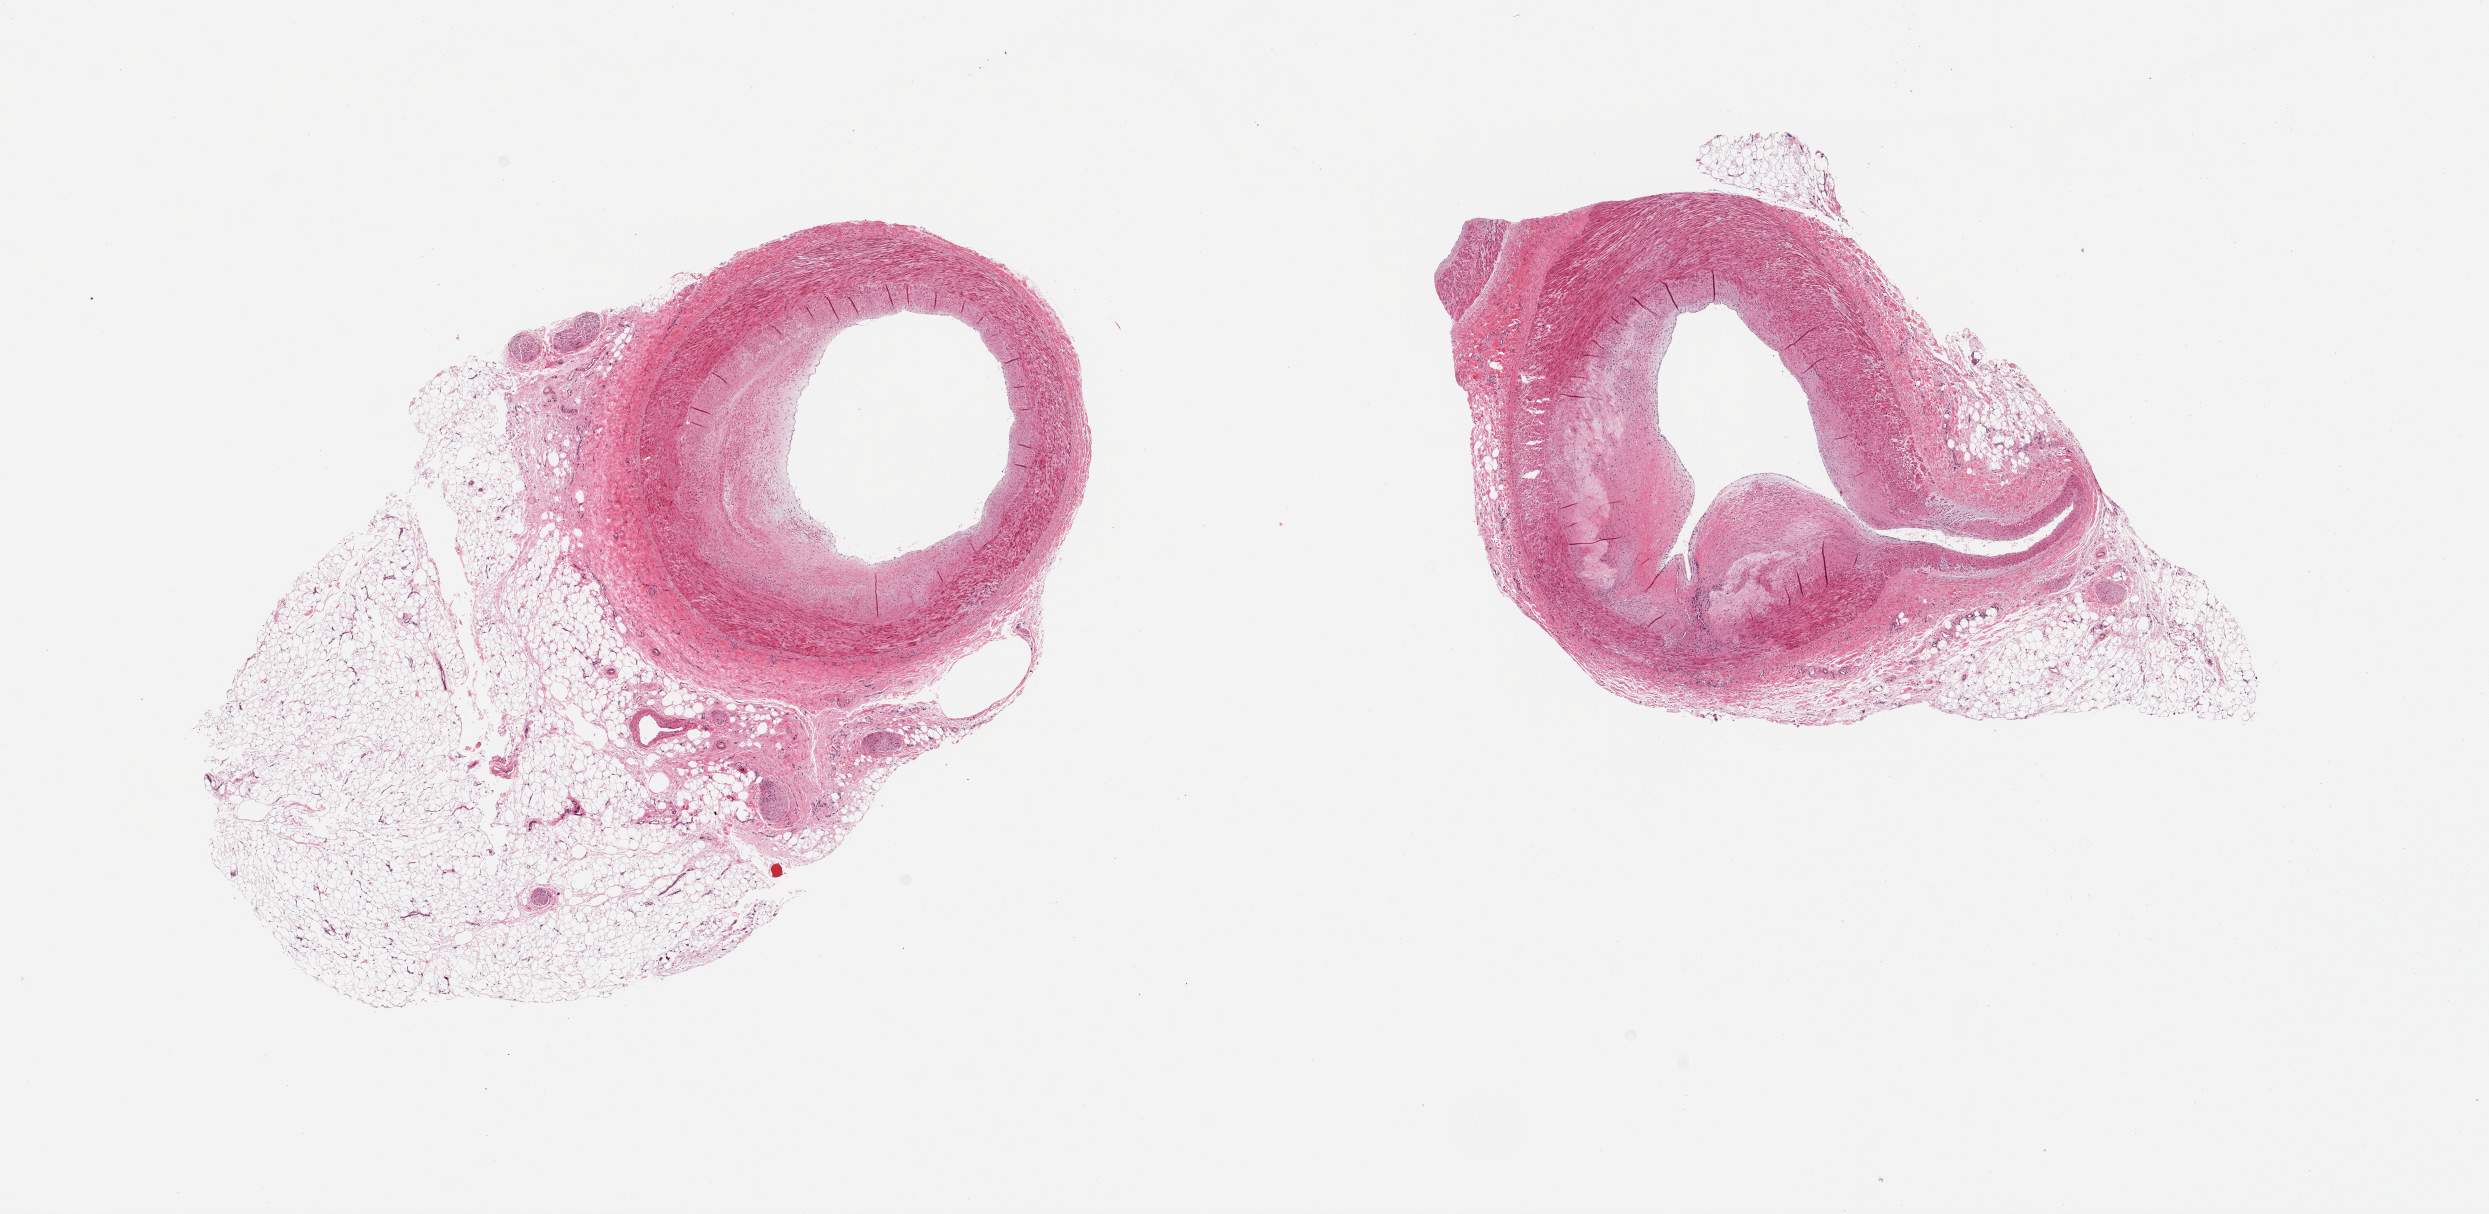
Whole-slide image, haematoxylin and eosin stain — whole scanned area (about 19.7 x 9.6 mm) shown as a low-resolution overview; PAXgene-fixed paraffin-embedded (PFPE) section; sampled site (target tissue): coronary artery; donor tissue sample. Male donor.
Review note (as recorded): 2 pieces; atheroma narrowing lumen up to 50-75%, adherent adipose and fibrovascular tissue with nerves up to 3.6mm.